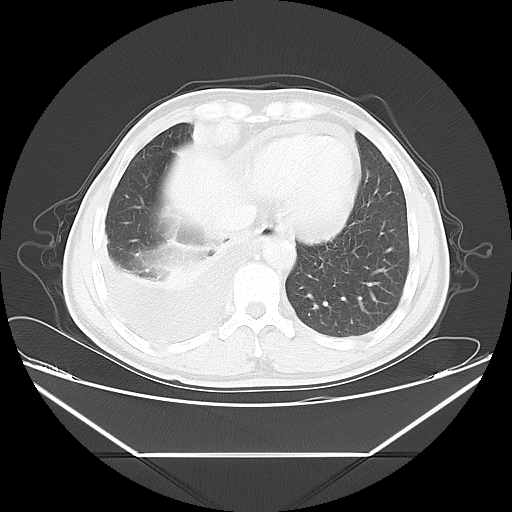
Chest CT, one axial slice; slice 13 of 56 in the series (ordered by position); reconstruction kernel LUNG; lung window (W 1500 / L -600 HU); 512 × 512 image matrix, field of view 412 × 412 mm. Patient: male, 57 years. Case-level facts recorded for this patient, not image findings: clinical TNM (as recorded): T2 N3 M1.
Annotated regions visible in this slice (bounding box drawn by a radiologist):
- lung tumour (recorded histology: adenocarcinoma): bounding box (x1, y1, x2, y2) in pixels: (192, 109, 258, 157)